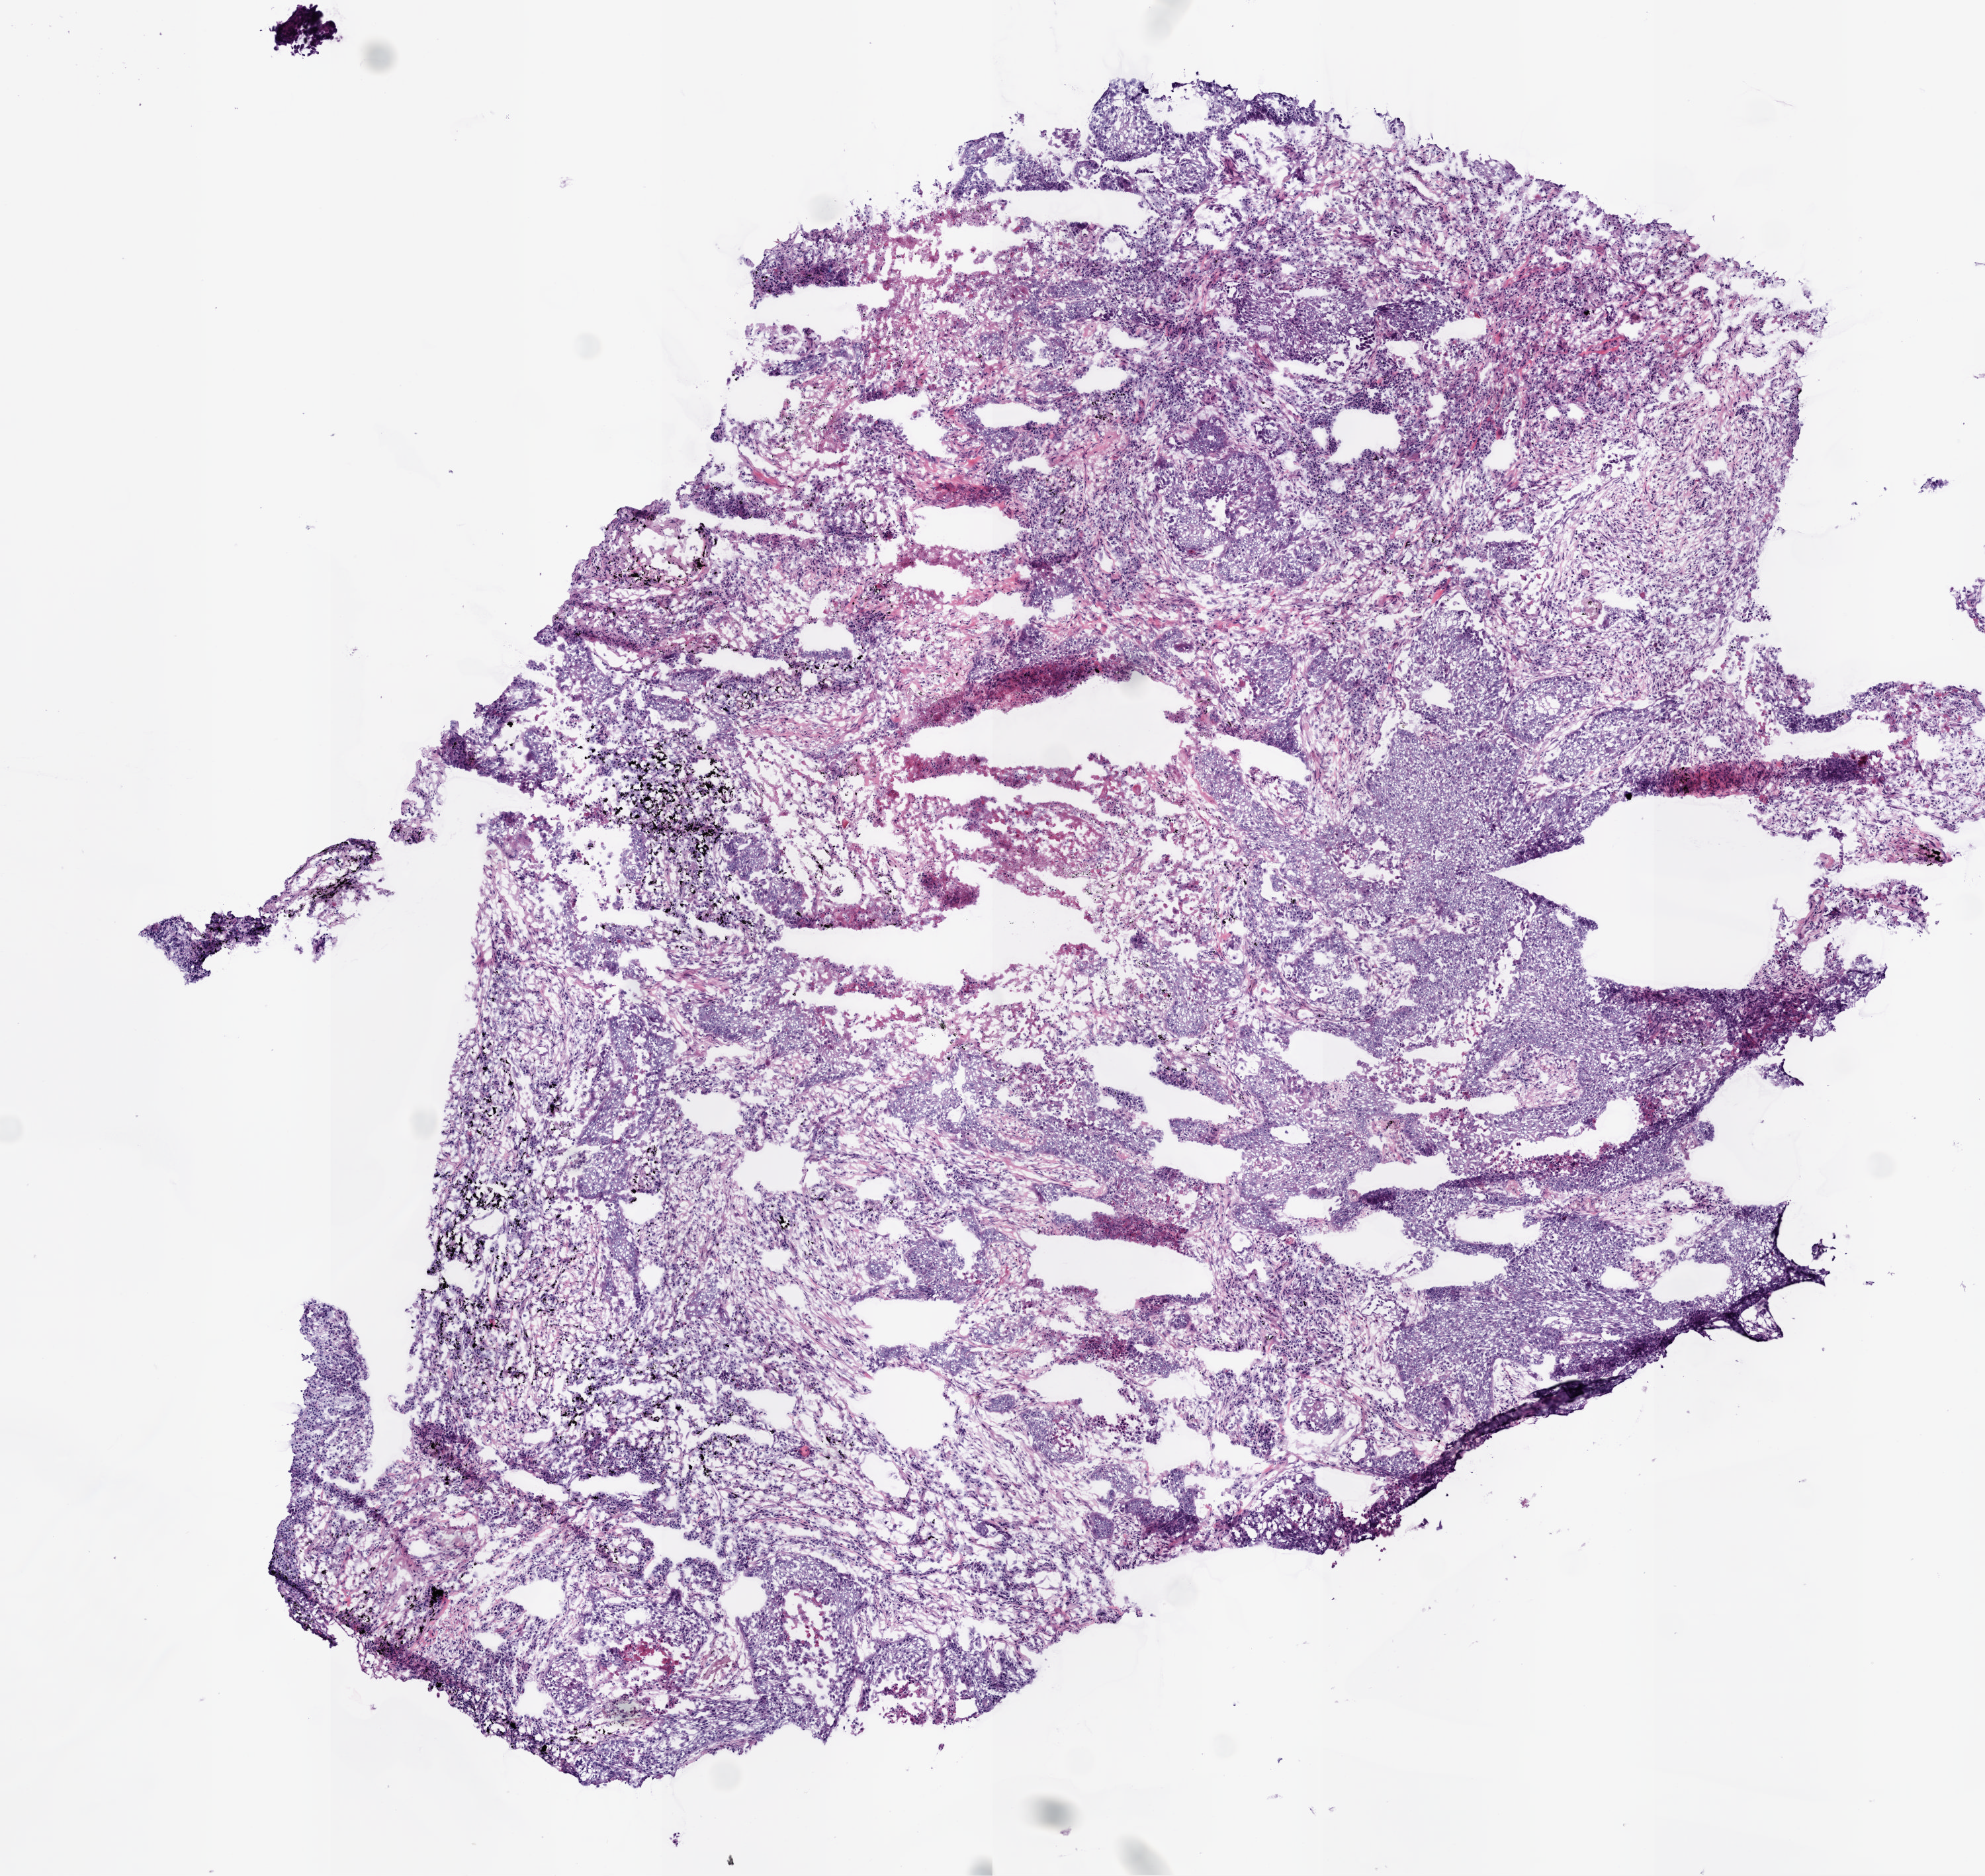
Whole-slide histology image, H&E-stained, shown as a low-resolution overview of the whole scanned area (about 6.0 x 5.7 mm, from a 20x scan). Frozen section from the bottom of the tissue portion. Sample: primary tumour, lung. Patient: male, age at initial diagnosis 72 years. Pathologist review of this section (percent, as recorded): tumour cells 70%, tumour nuclei 75%, normal cells 0%, stromal cells 15%, necrosis 15%. Infiltration values recorded for this section: lymphocyte infiltration 10%.
• histologic diagnosis: Squamous cell carcinoma, NOS (upper lobe, lung)
• AJCC pathologic stage: IB